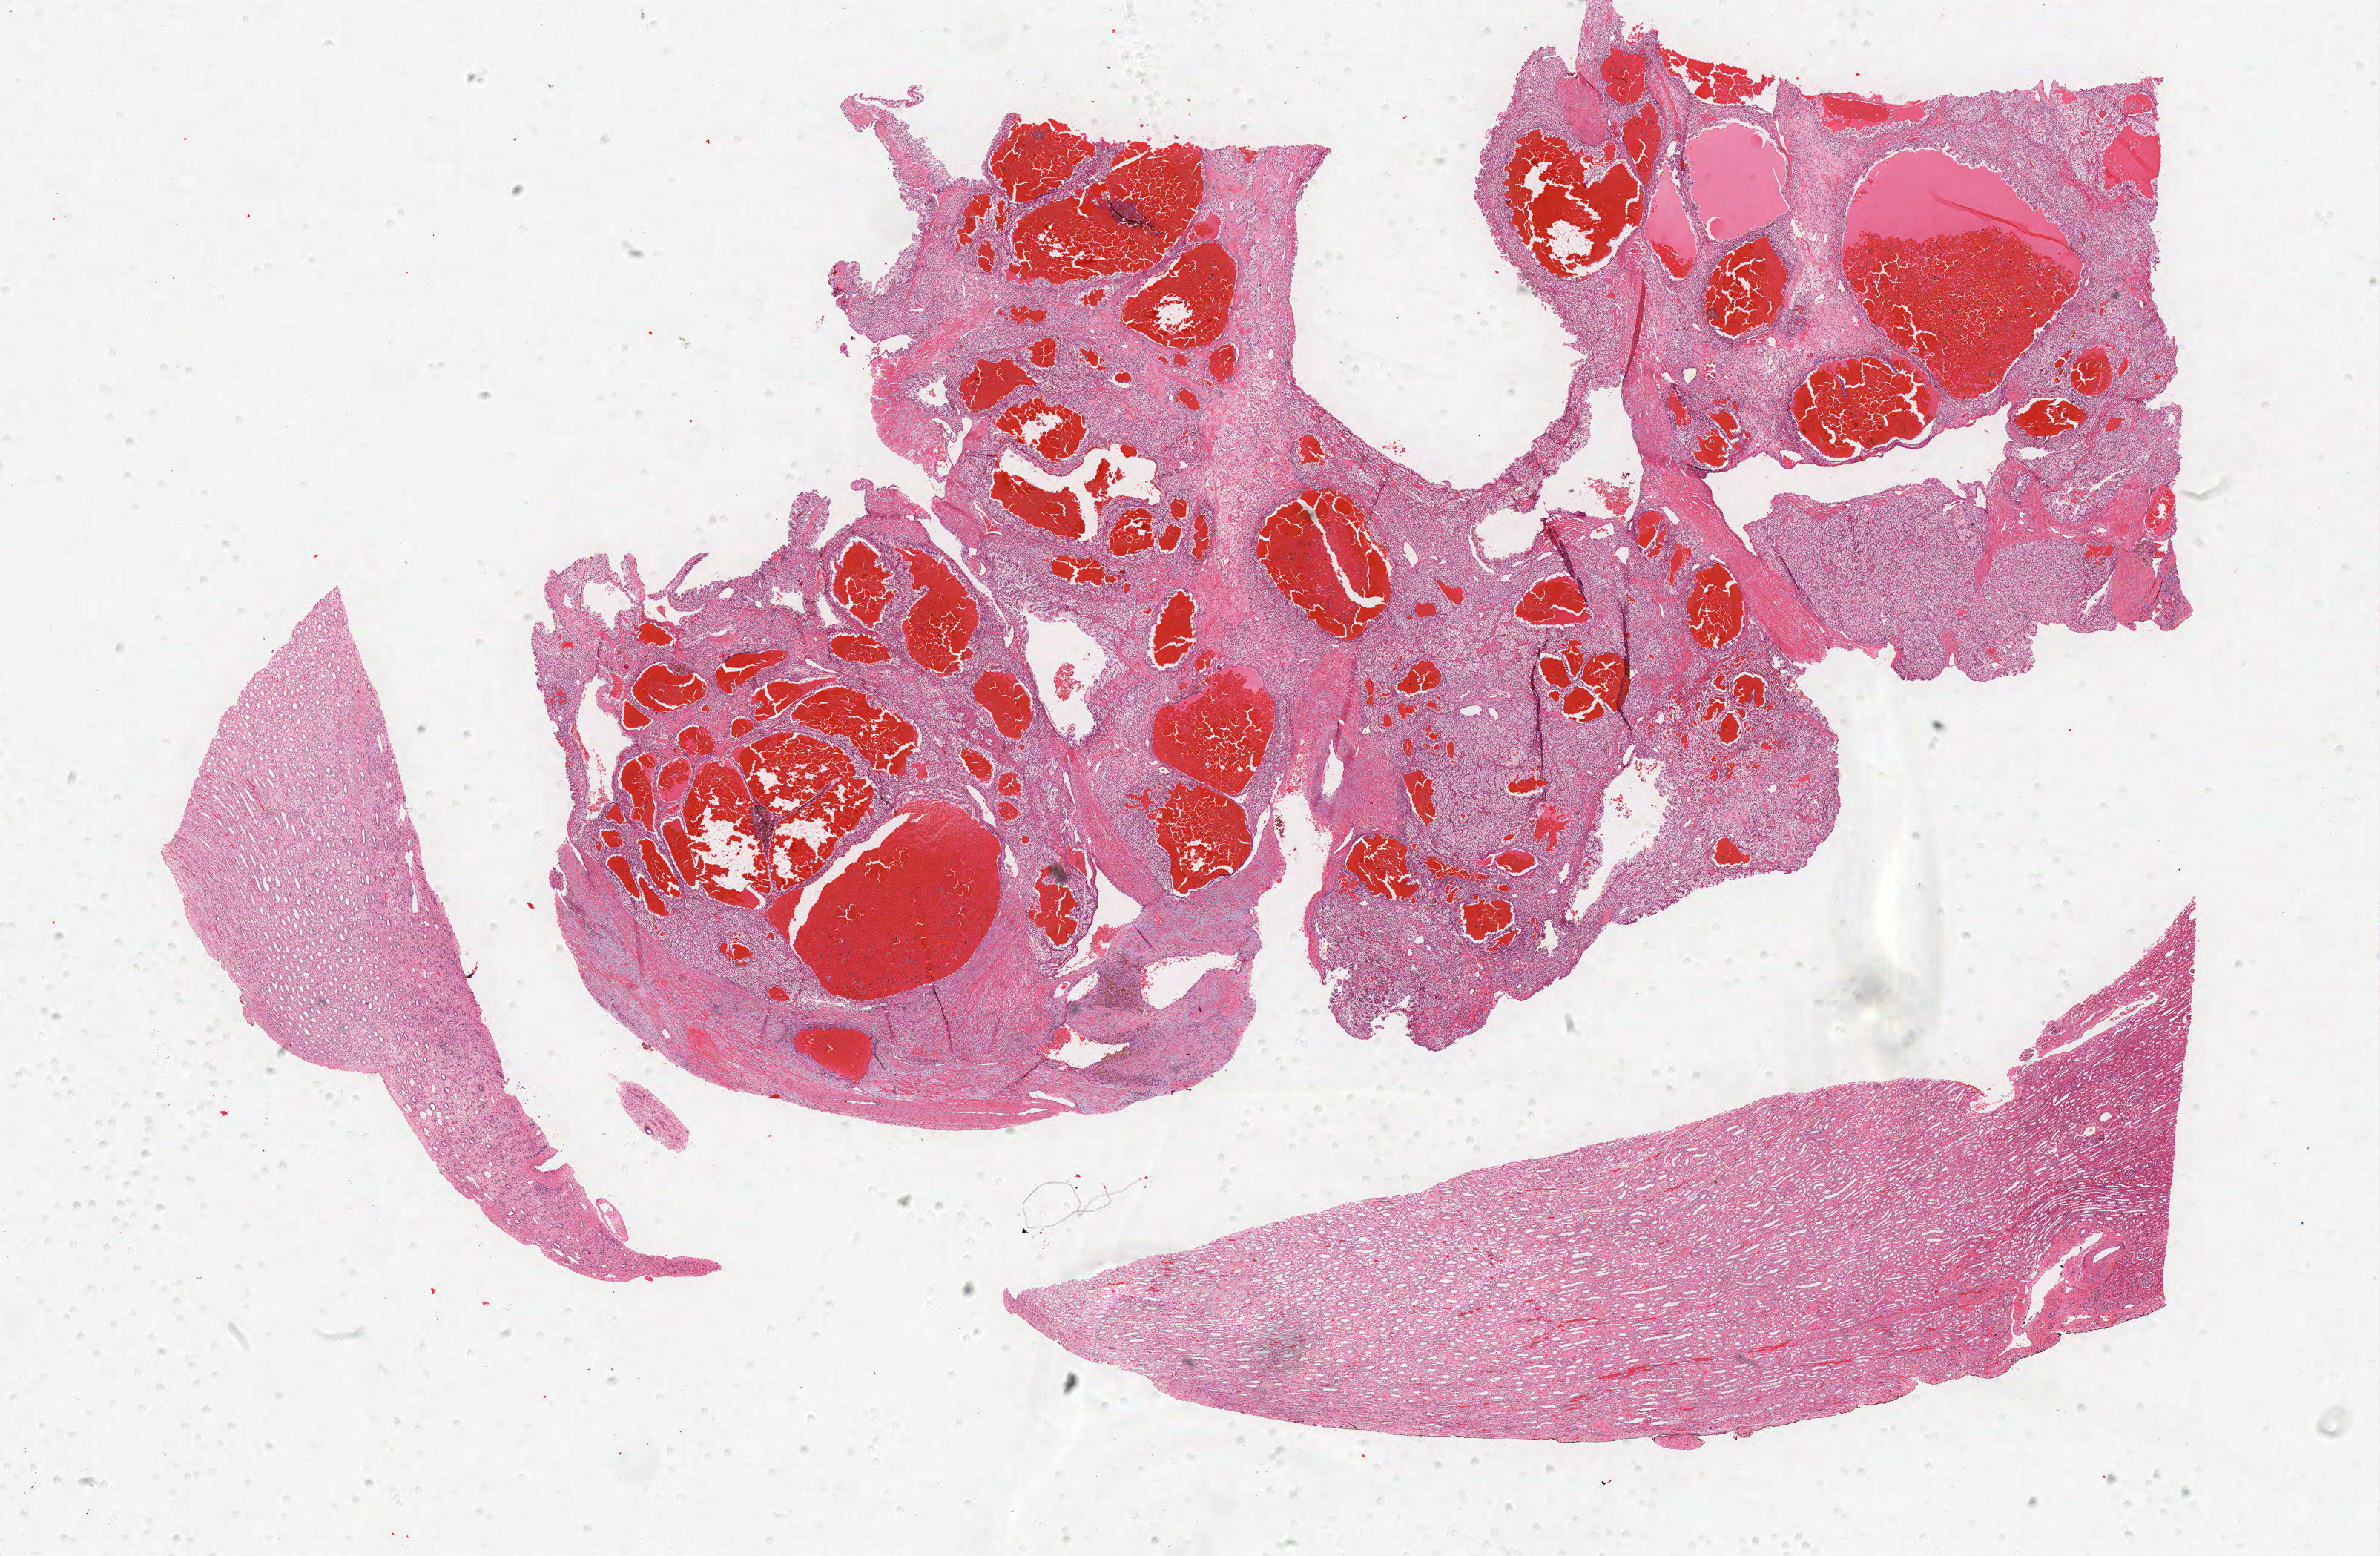
H&E whole-slide image, shown as a low-resolution overview of the whole scanned area (about 25.7 x 16.8 mm, slide scanned at 40x), formalin-fixed paraffin-embedded (FFPE) diagnostic section, sample: primary tumour, kidney. Patient: male, age at initial diagnosis 36 years. Histologic grade: G2 (moderately differentiated).
Histologic diagnosis: Clear cell adenocarcinoma, NOS. Laterality: left. AJCC pathologic stage: III.